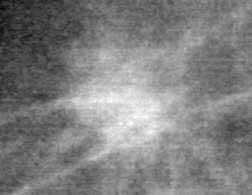
Region of interest cut from a scanned film mammogram (one marked finding), left breast, CC view.
- Mass, shape oval, margins ill defined; BI-RADS assessment category 4; pathology result (as recorded, not read from the image): malignant.